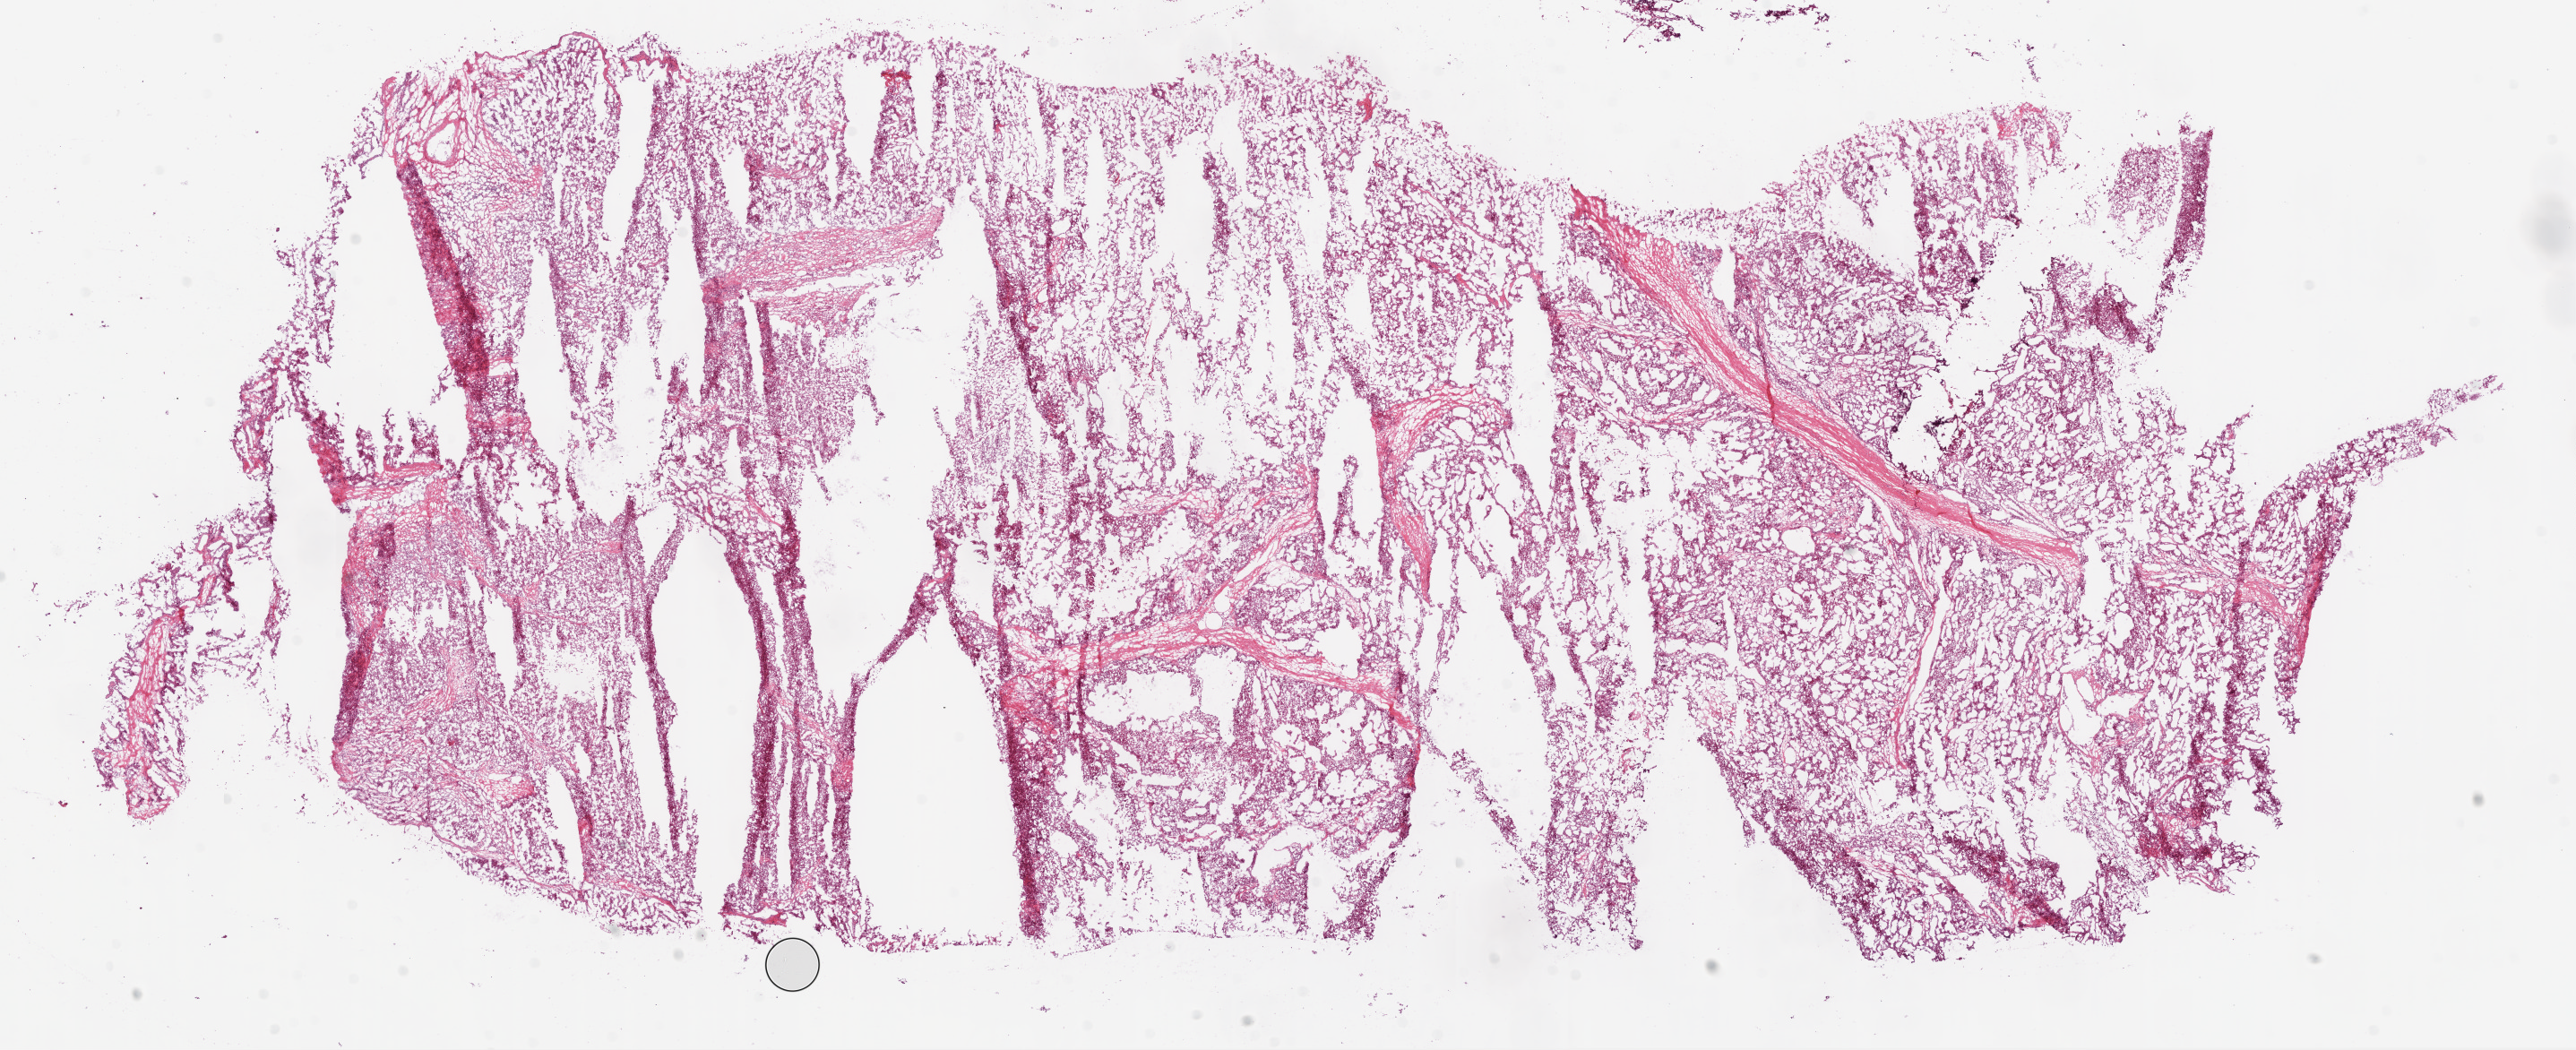
H&E whole-slide image, whole scanned area (about 23.1 x 9.4 mm) shown as a low-resolution overview; frozen section; primary tumour sample from the kidney. Patient: female, age at initial diagnosis 46 years. Histologic grade: G4 (undifferentiated). Composition of this section per pathologist review: tumour cells 95%, tumour nuclei 80%, normal cells 0%, stromal cells 5%, necrosis 0%.
TNM: T3a N1 M1. Histologic diagnosis: Clear cell adenocarcinoma, NOS. AJCC pathologic stage: IV.